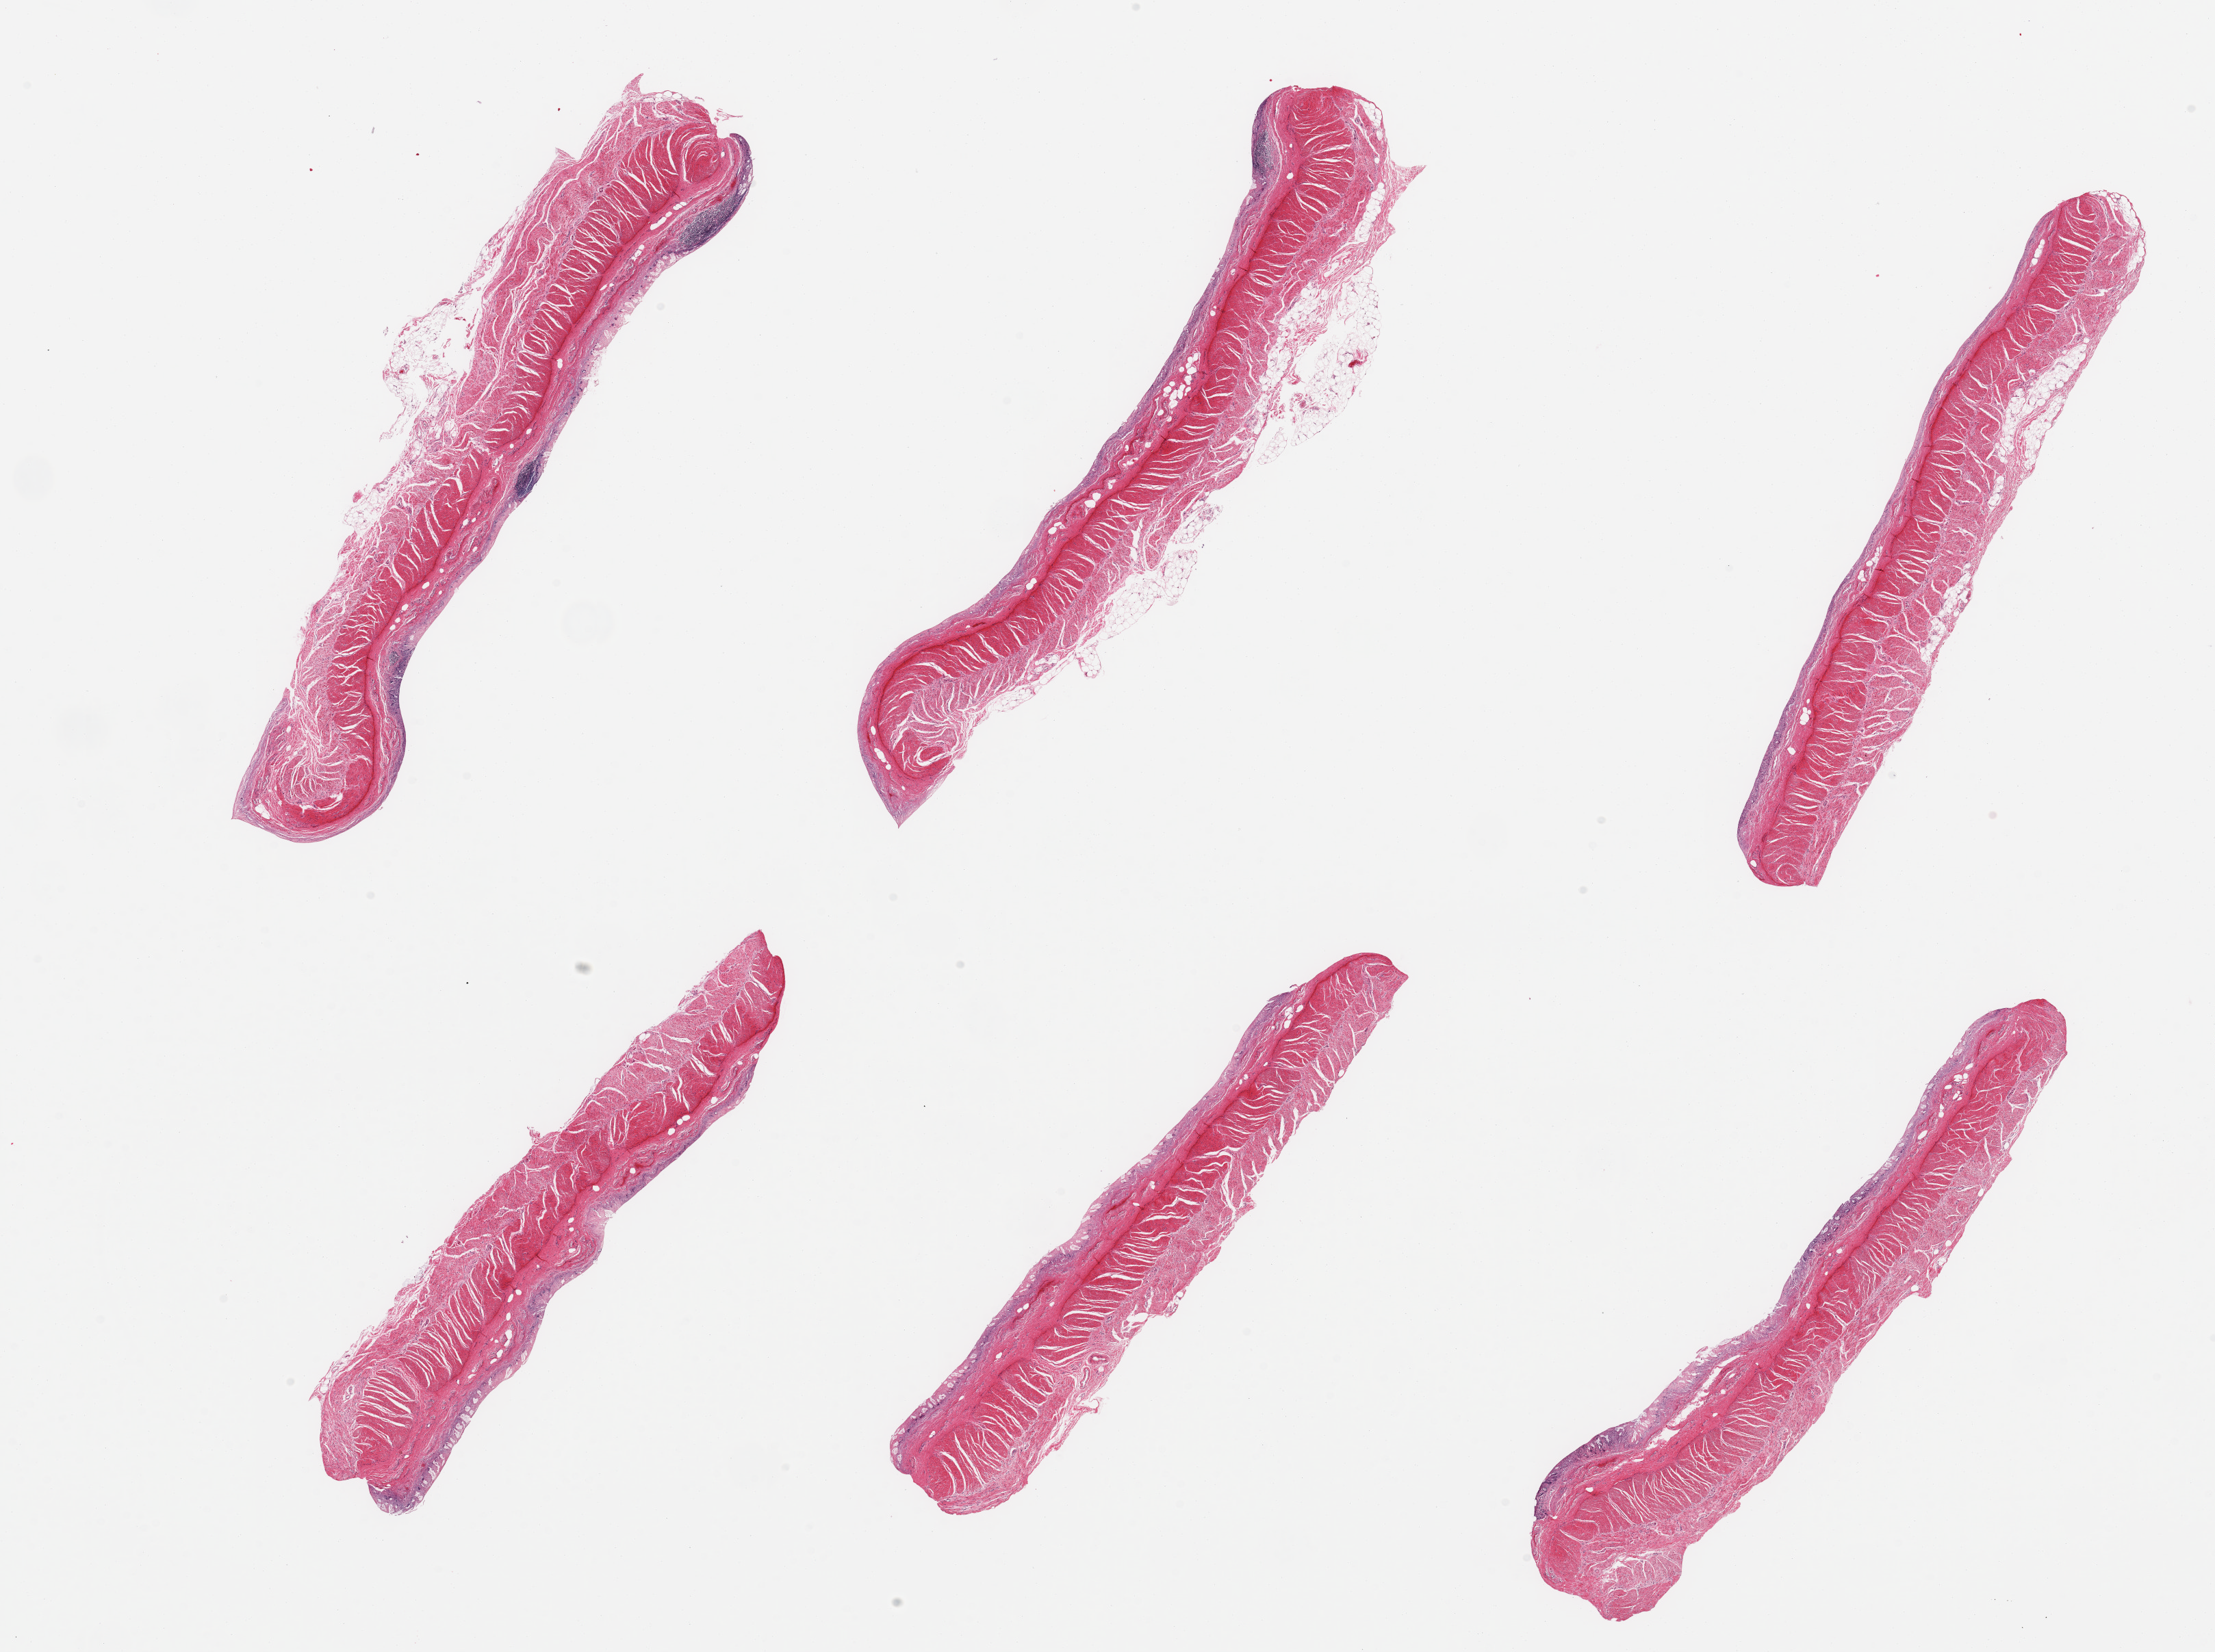
Haematoxylin and eosin whole-slide image, whole scanned area (about 25.6 x 19.1 mm, from a 20x scan) shown as a low-resolution overview; PAXgene-fixed, paraffin-embedded tissue; section of ileum (target tissue); donor tissue sample. Donor: male.
Review note (as recorded): 6 pieces; epithelium totally autolyzed and ~5% tissue is residual lymphoid aggregates, muscularis (not target) also present.